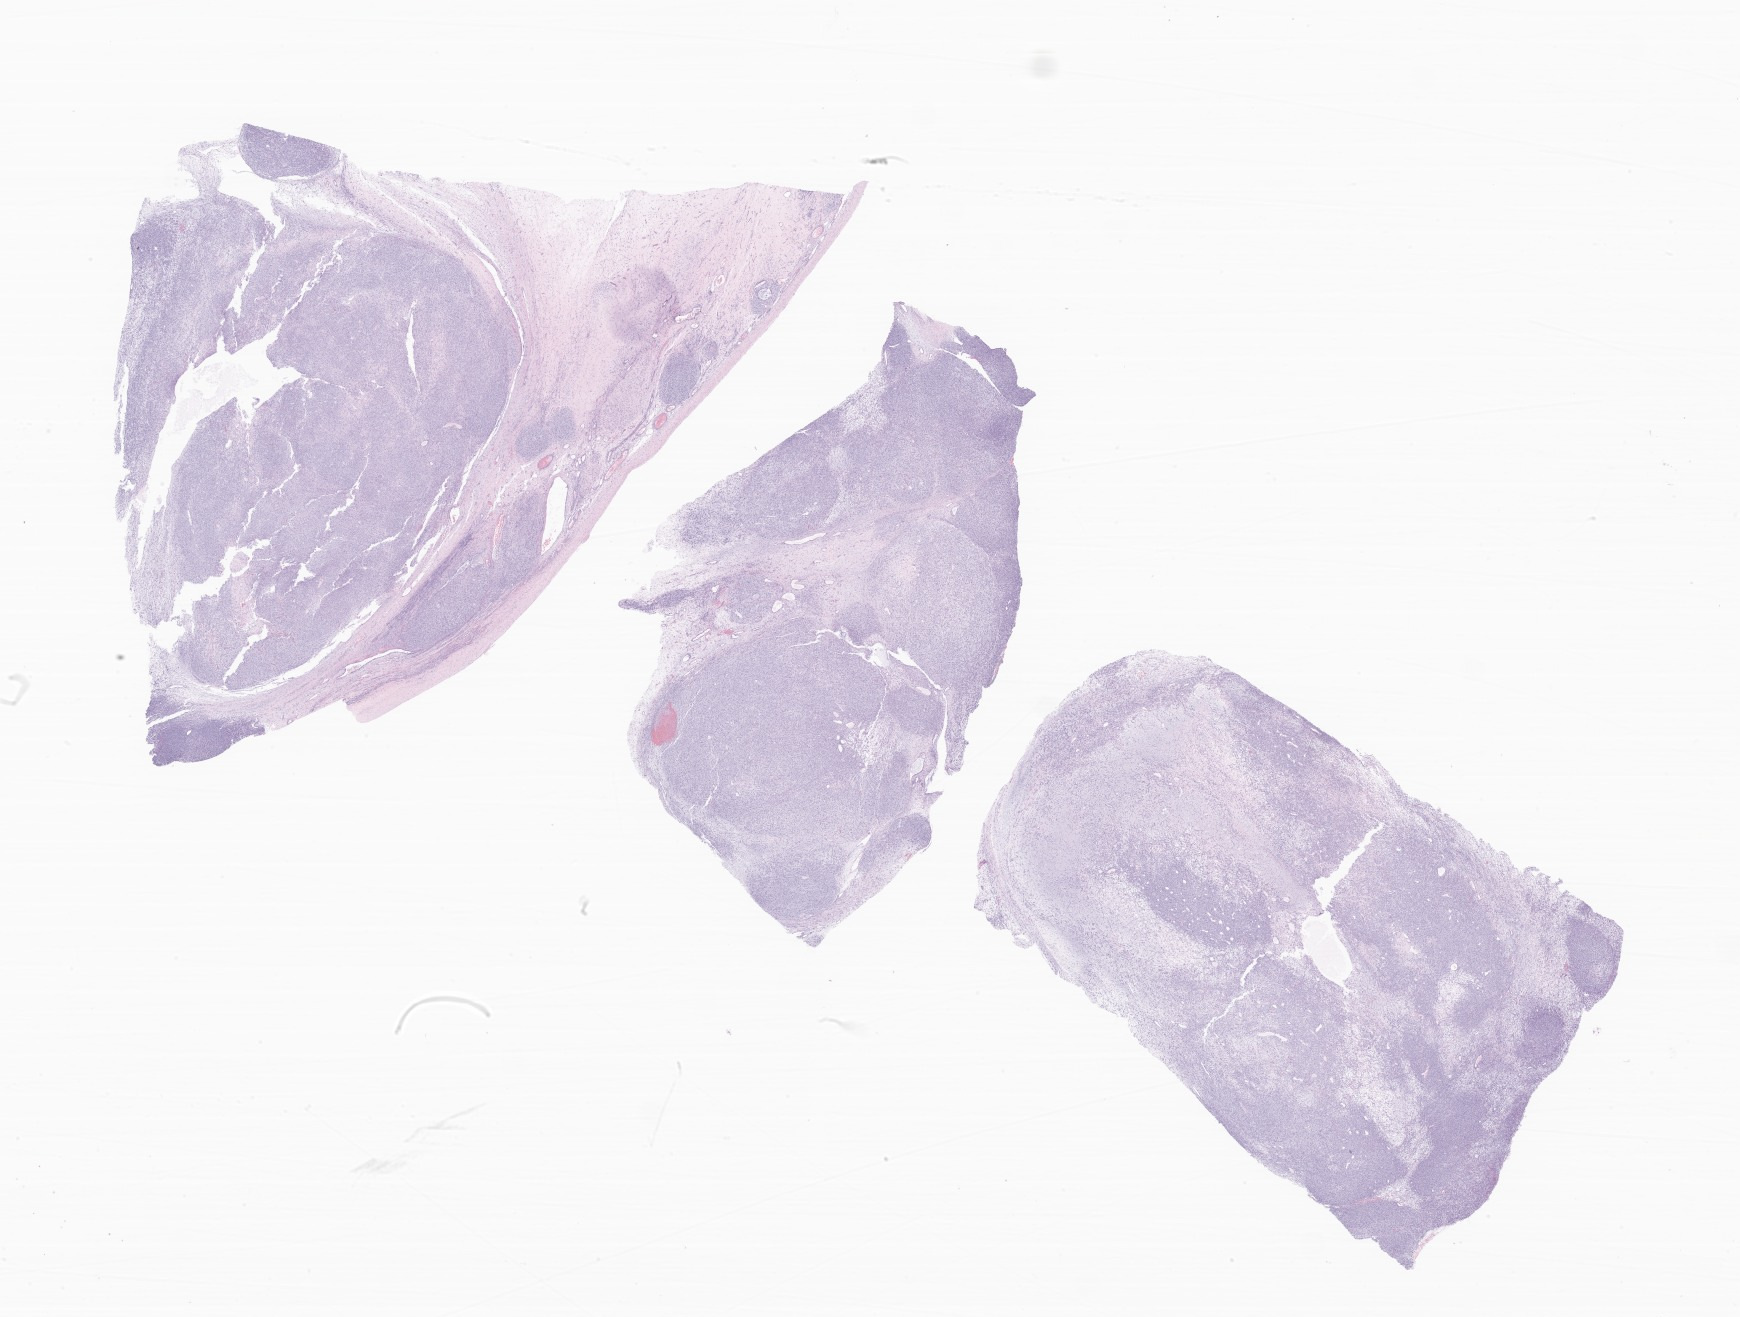
Hematoxylin and eosin (H&E) whole-slide image of tumor tissue from the ovary, whole scanned area (about 29.3 x 22.2 mm) shown as a low-resolution overview; FFPE section. Patient female; age 193 months (16 years 1 month).
Diagnosis: Sex cord-gonadal stromal tumor, NOS.